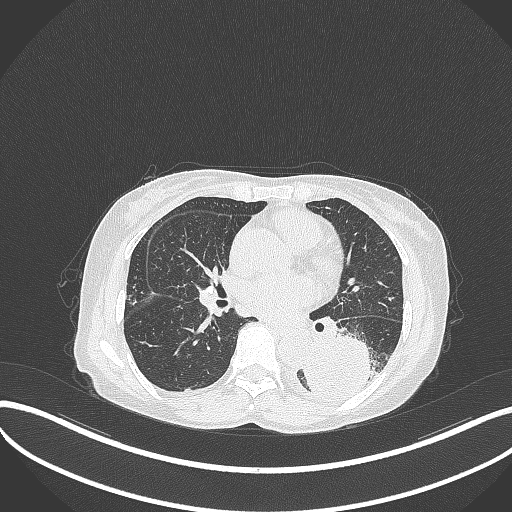
Chest CT, one axial slice. Position 152 of 370 along the scan axis. Lung window (W 1500 / L -600 HU). 1 mm slice thickness. 512 × 512 image matrix, field of view 400 × 400 mm. Patient: female, 78 years. From the clinical record (not read from this slice): clinical TNM (as recorded): T3 N0 M1.
Outlined on this slice (bounding box drawn by a radiologist):
- lung tumour (recorded histology: squamous cell carcinoma): bounding box (x1, y1, x2, y2) in pixels: (299, 325, 388, 403)